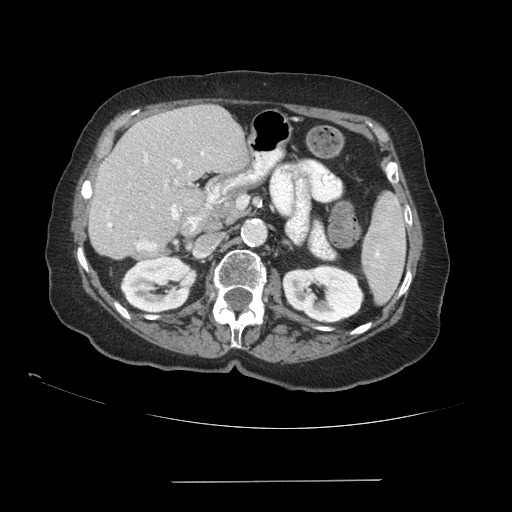
Contrast-enhanced abdominal CT (liver protocol), one axial slice. Position 47 of 89 along the scan axis. Reconstruction kernel STANDARD. 140 kVp. Soft-tissue window (W 400 / L 40 HU). 2.5 mm slice thickness. 512 × 512 image matrix, field of view 400 × 400 mm. From the clinical record (not read from this slice): diagnosis: hepatocellular carcinoma (patient treated with transarterial chemoembolisation; whether this scan precedes or follows treatment is not stated here); TNM stage (as recorded): Stage-IVA.
Structures marked on this image (semi-automatically segmented with operator editing):
- liver parenchyma outside the tumour (the mass and vessels are separate outlines, so this box may not span the whole liver): bounding box (x1, y1, x2, y2) in pixels: (88, 104, 246, 258)
- liver vessels: (107, 151, 211, 251)